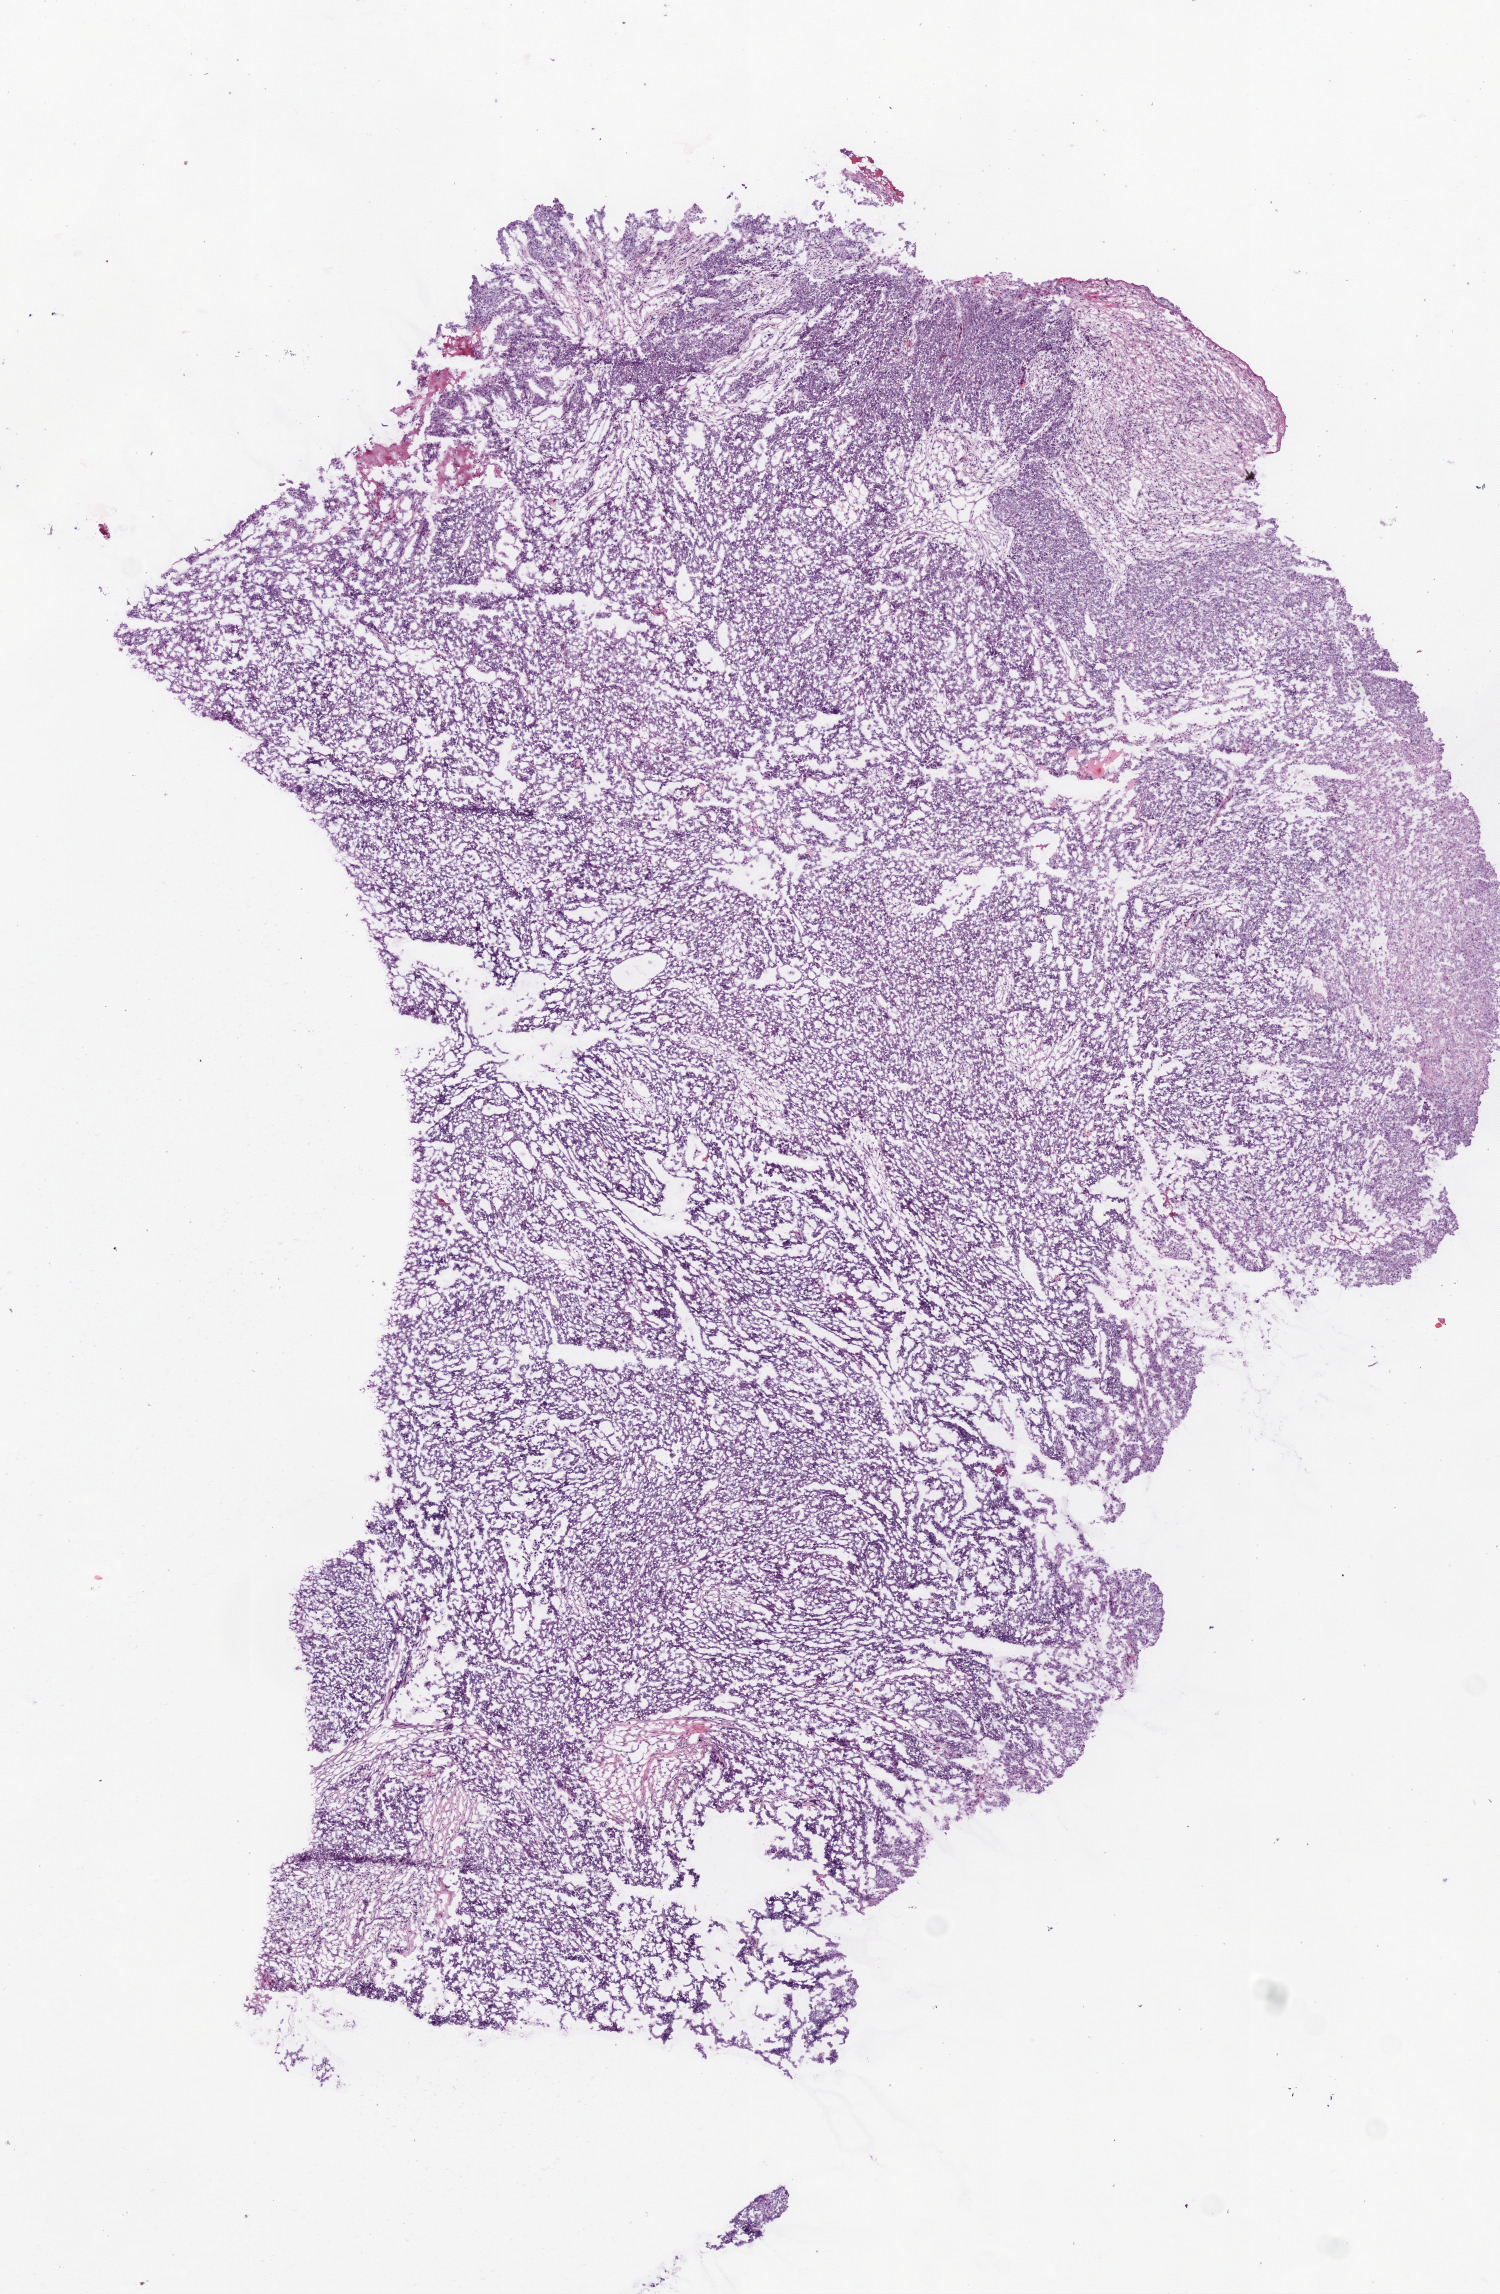
Digitized H&E tissue section (whole slide) — low-resolution overview of the scanned area, about 6.0 x 9.2 mm, frozen section from the bottom of the tissue portion, sample: primary tumour, ovary. Female patient; age at initial diagnosis 46 years. Histologic grade: G3 (poorly differentiated). Pathologist review of this section (percent, as recorded): tumour cells 89%, tumour nuclei 90%, normal cells 0%, stromal cells 10%, necrosis 1%.
* pathologic diagnosis: Serous cystadenocarcinoma, NOS
* FIGO stage: IIIC